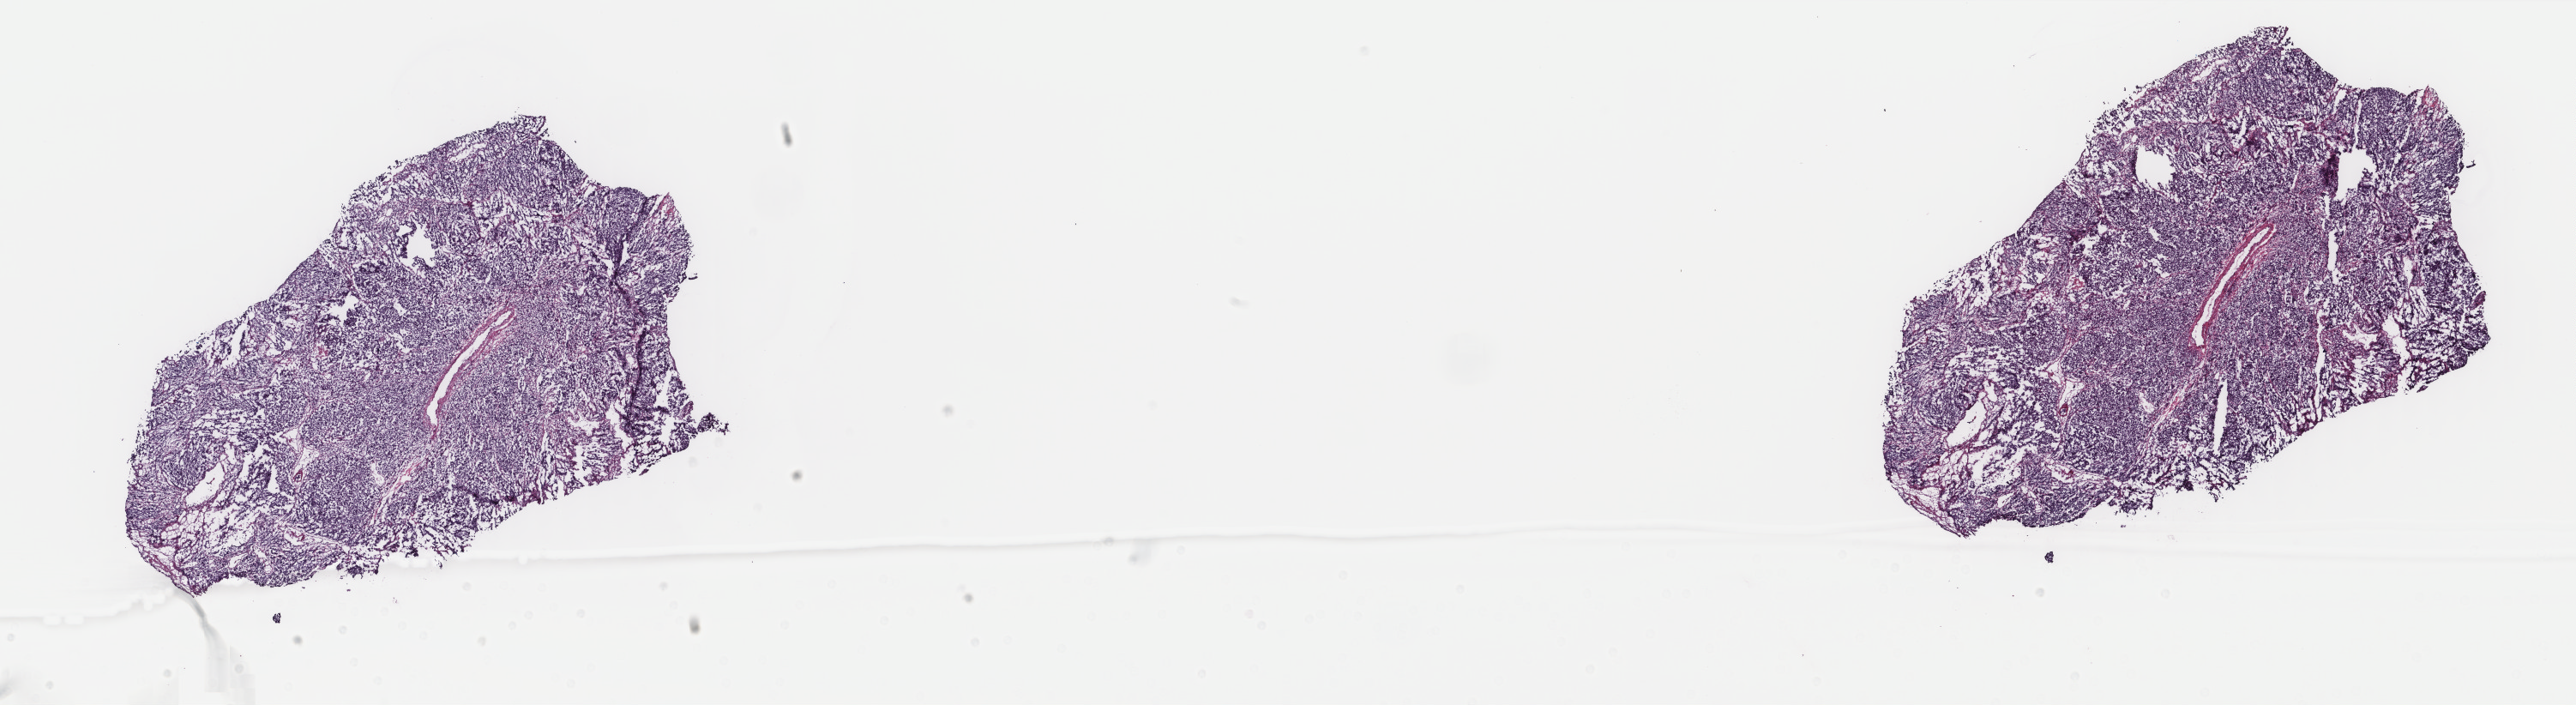
Digitized H&E tissue section (whole slide), shown as a low-resolution overview of the whole scanned area (about 23.8 x 6.5 mm); frozen section from the top of the tissue portion; primary tumour sample from the cervix. Female patient; age at initial diagnosis 28 years. Composition of this section per pathologist review: tumour cells 80%, tumour nuclei 80%.
Histologic diagnosis: Basaloid squamous cell carcinoma (cervix uteri).